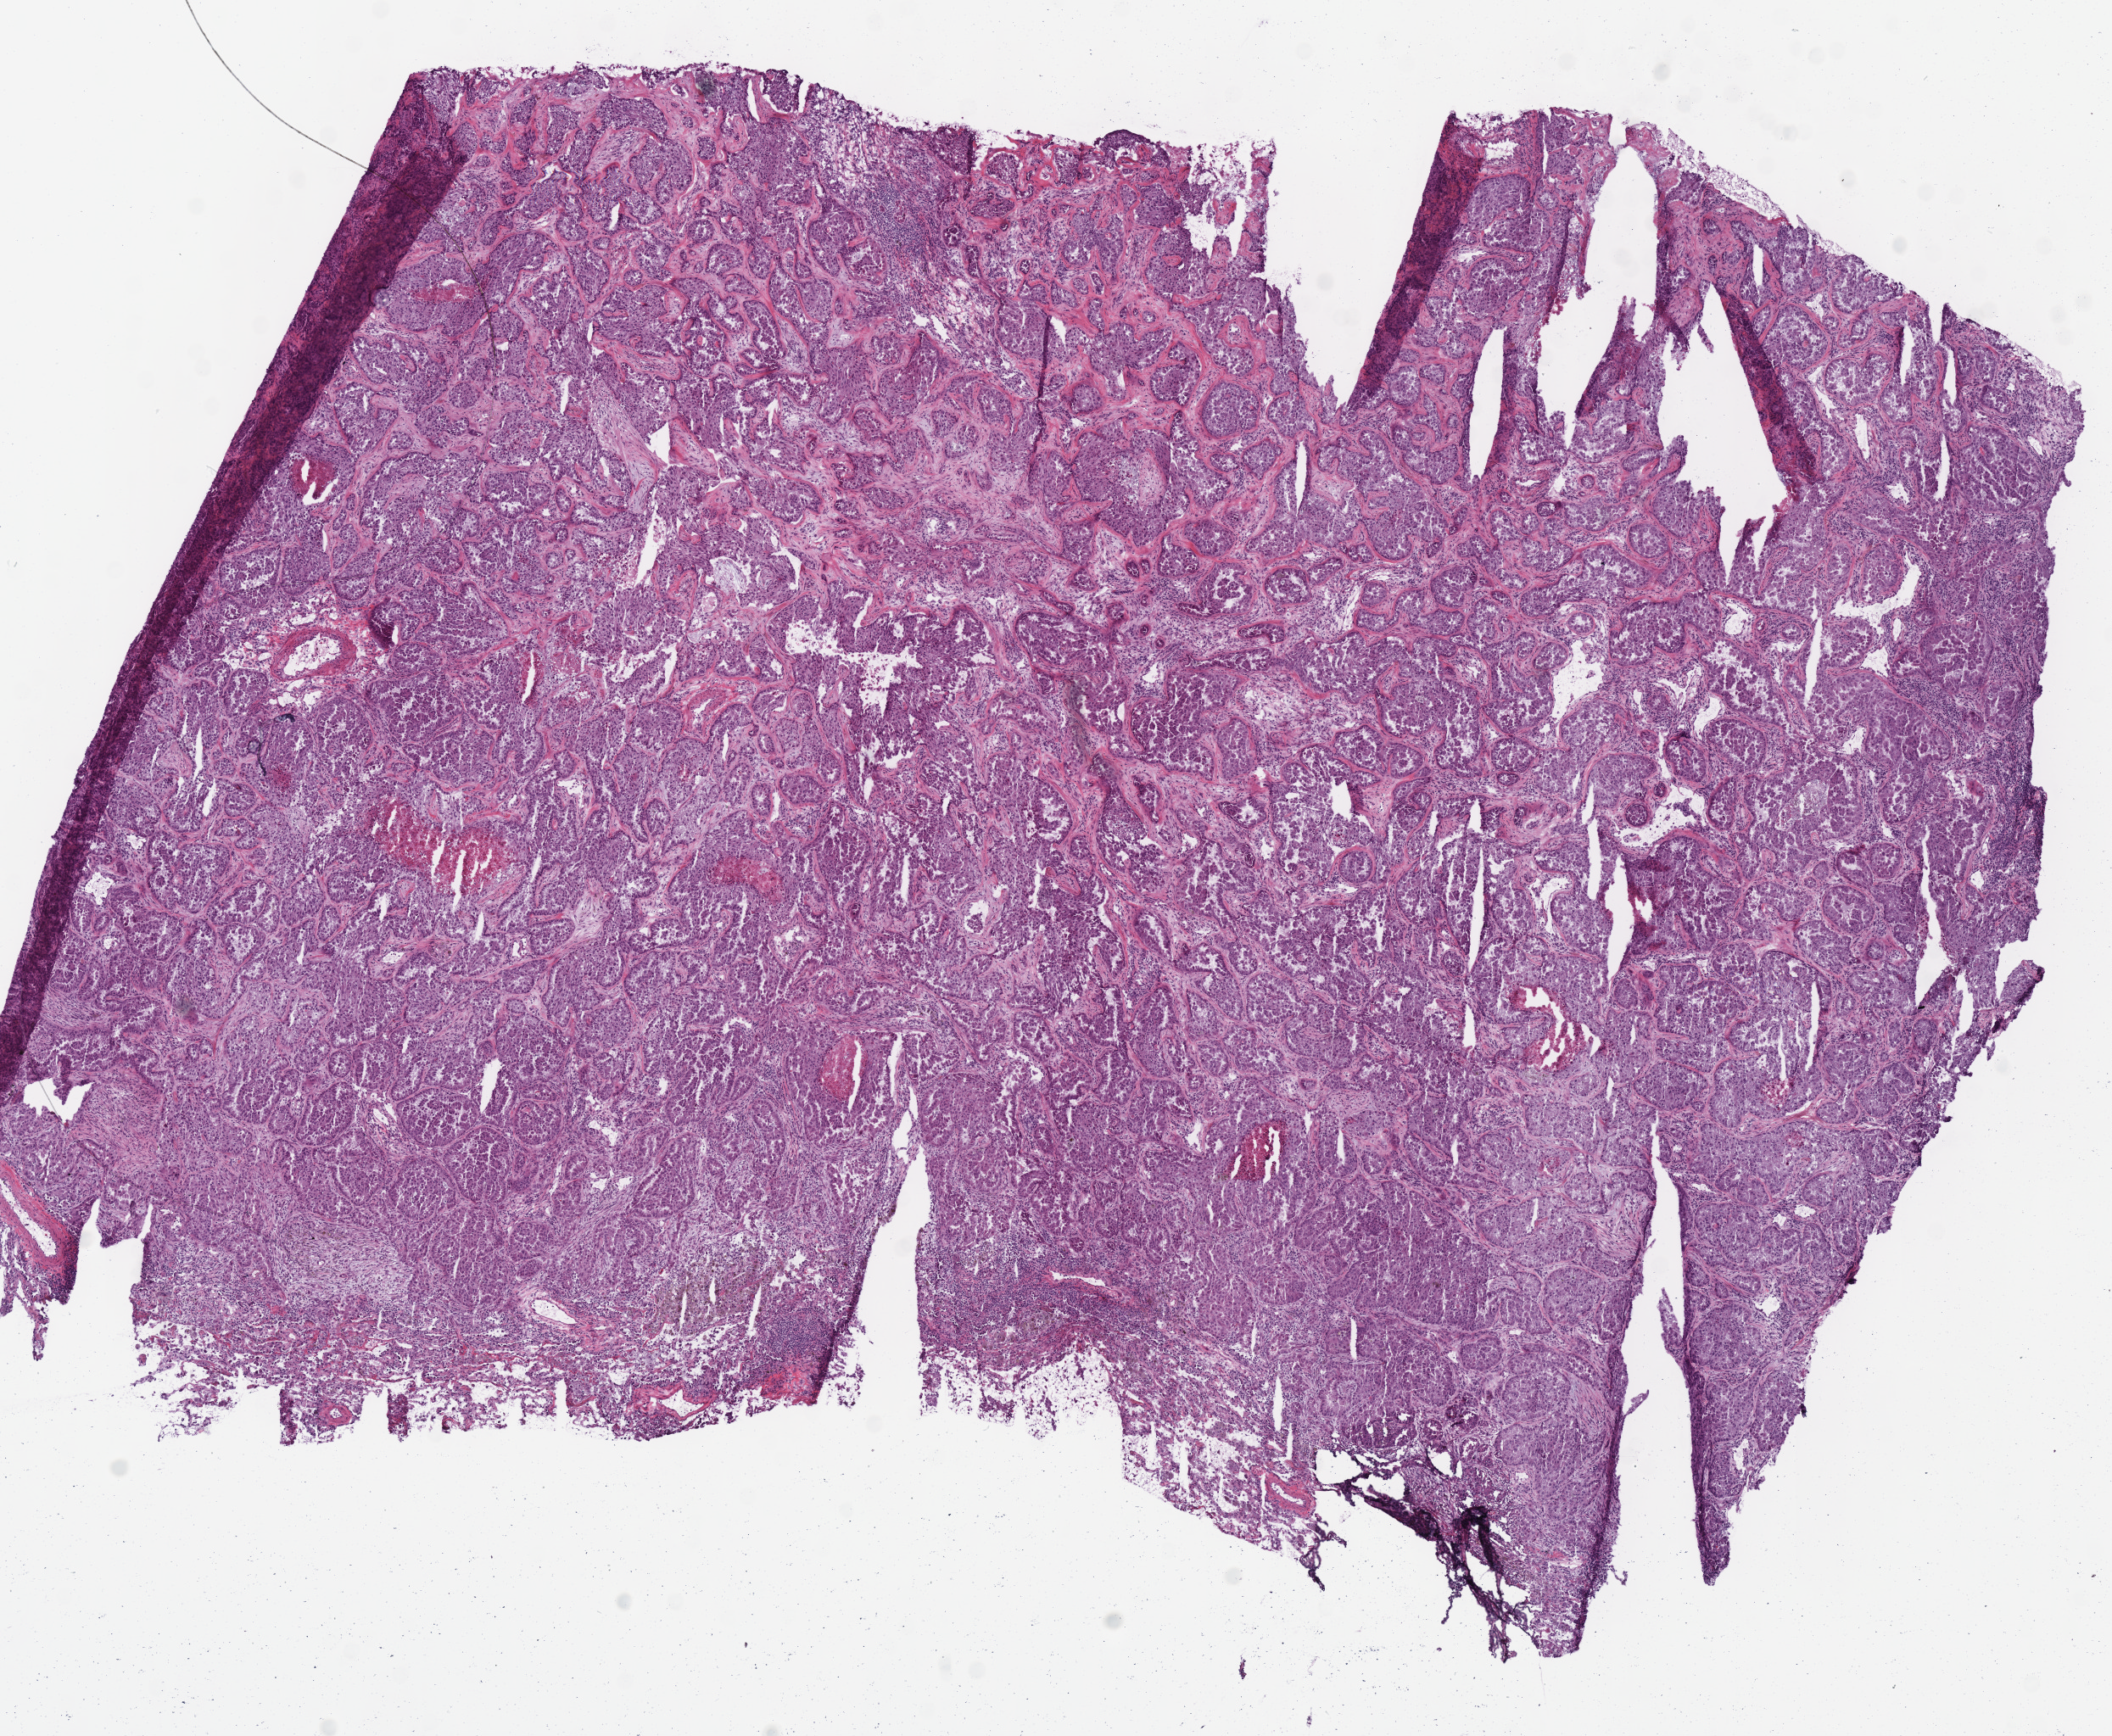
Whole-slide histology image, H&E, a low-resolution overview of the entire scanned area, about 9.8 x 8.0 mm (slide scanned at 40x); frozen section; sample: primary tumour, lung. Female, age 54 years at initial diagnosis. Slide review estimates, as recorded: tumour cells 96%, tumour nuclei 80%, normal cells 0%, stromal cells 0%, necrosis 4%. Inflammatory infiltration, as recorded: lymphocyte infiltration 12%, monocyte infiltration 0%, neutrophil infiltration 0%.
Laterality: right. AJCC pathologic stage: IB. Histologic diagnosis: Adenocarcinoma, NOS (upper lobe, lung).